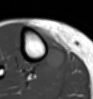
MRI of an extremity soft-tissue mass, one axial slice. MR volume resampled by the dataset authors to the PET/CT grid (not the native acquisition matrix). 3.27 mm slice thickness. 93 × 99 image matrix, field of view 91 × 97 mm. Female patient. From the clinical record (not read from this slice): histological type: undifferentiated – high grade; grade: high; site of the primary tumour: right thigh.
Annotated regions visible in this slice (expert contour drawn on MRI and transferred to this co-registered scan by the dataset authors):
- gross tumour volume (mass): bounding box (x1, y1, x2, y2) in pixels: (34, 27, 64, 71)